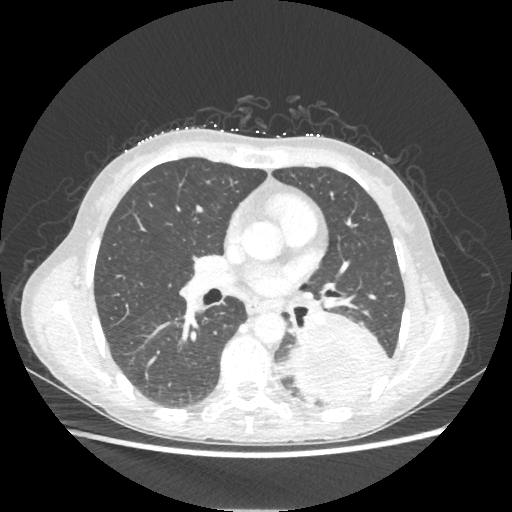
Chest CT, one axial slice; position 118 of 221 along the scan axis; reconstruction kernel STANDARD; lung window (W 1500 / L -600 HU); 512 × 512 image matrix. Patient: female, 53 years. Case-level facts recorded for this patient, not image findings: clinical TNM (as recorded): T3 N0 M0.
Structures marked on this image (rectangle marked by the reading radiologist):
- lung tumour (recorded histology: adenocarcinoma): bounding box (x1, y1, x2, y2) in pixels: (285, 308, 393, 404)